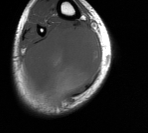
MRI of an extremity soft-tissue mass, one axial slice. Slice 40 of 76 in the series (ordered by position). MR volume resampled by the dataset authors to the PET/CT grid (not the native acquisition matrix). 3.27 mm slice thickness. 148 × 133 image matrix, field of view 145 × 130 mm. Male patient. From the clinical record (not read from this slice): histological type: liposarcoma - round cell; grade: high; site of the primary tumour: right calf.
Outlined on this slice (expert contour drawn on MRI and transferred to this co-registered scan by the dataset authors):
- gross tumour volume (mass): bounding box (x1, y1, x2, y2) in pixels: (24, 26, 101, 109)